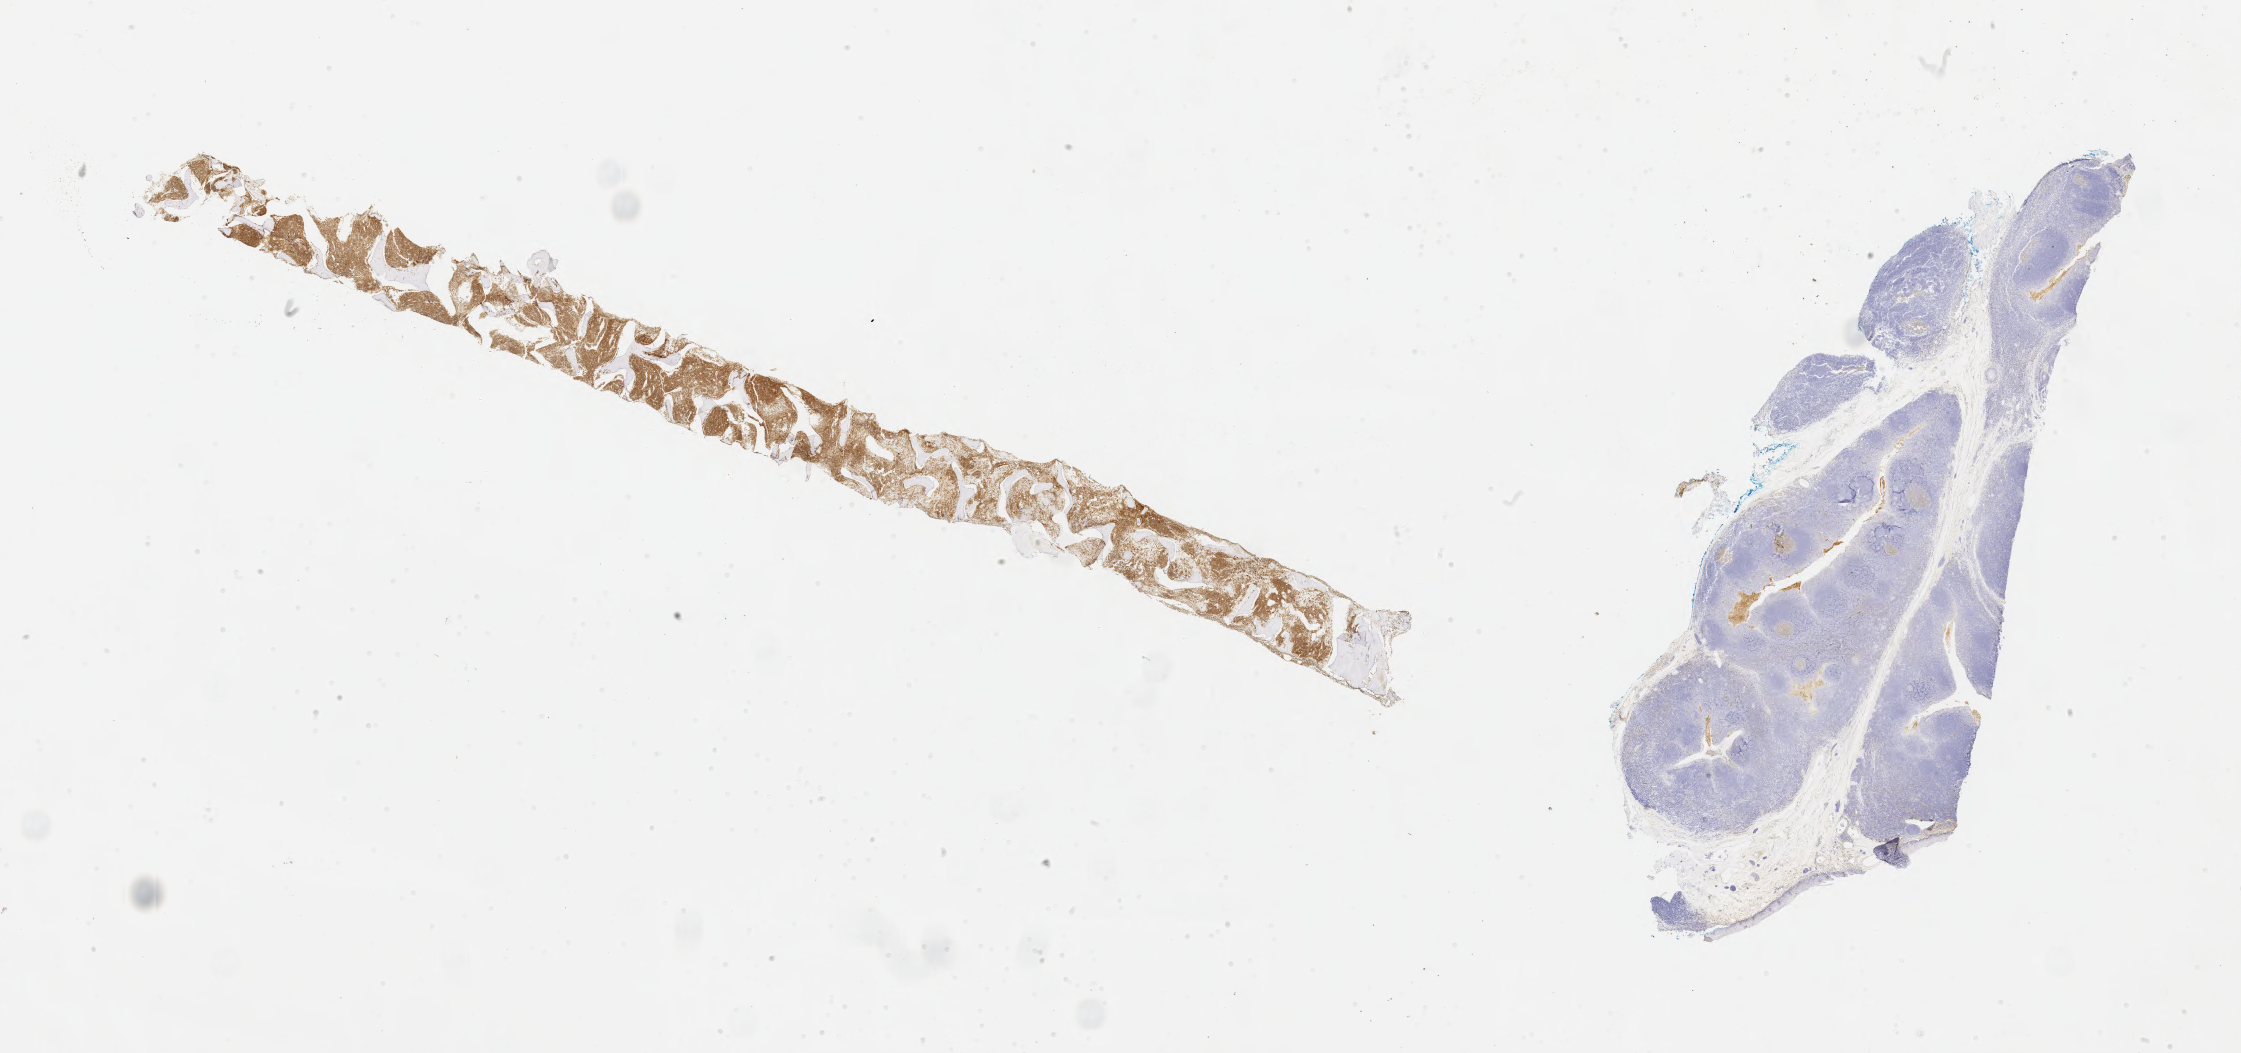
IHC for CD10, whole-slide image, shown as a low-resolution overview of the whole scanned area (about 36.2 x 17.0 mm). Tumor tissue. Site: bone marrow. Male patient, 18 years old.
- histologic diagnosis: Burkitt lymphoma, NOS